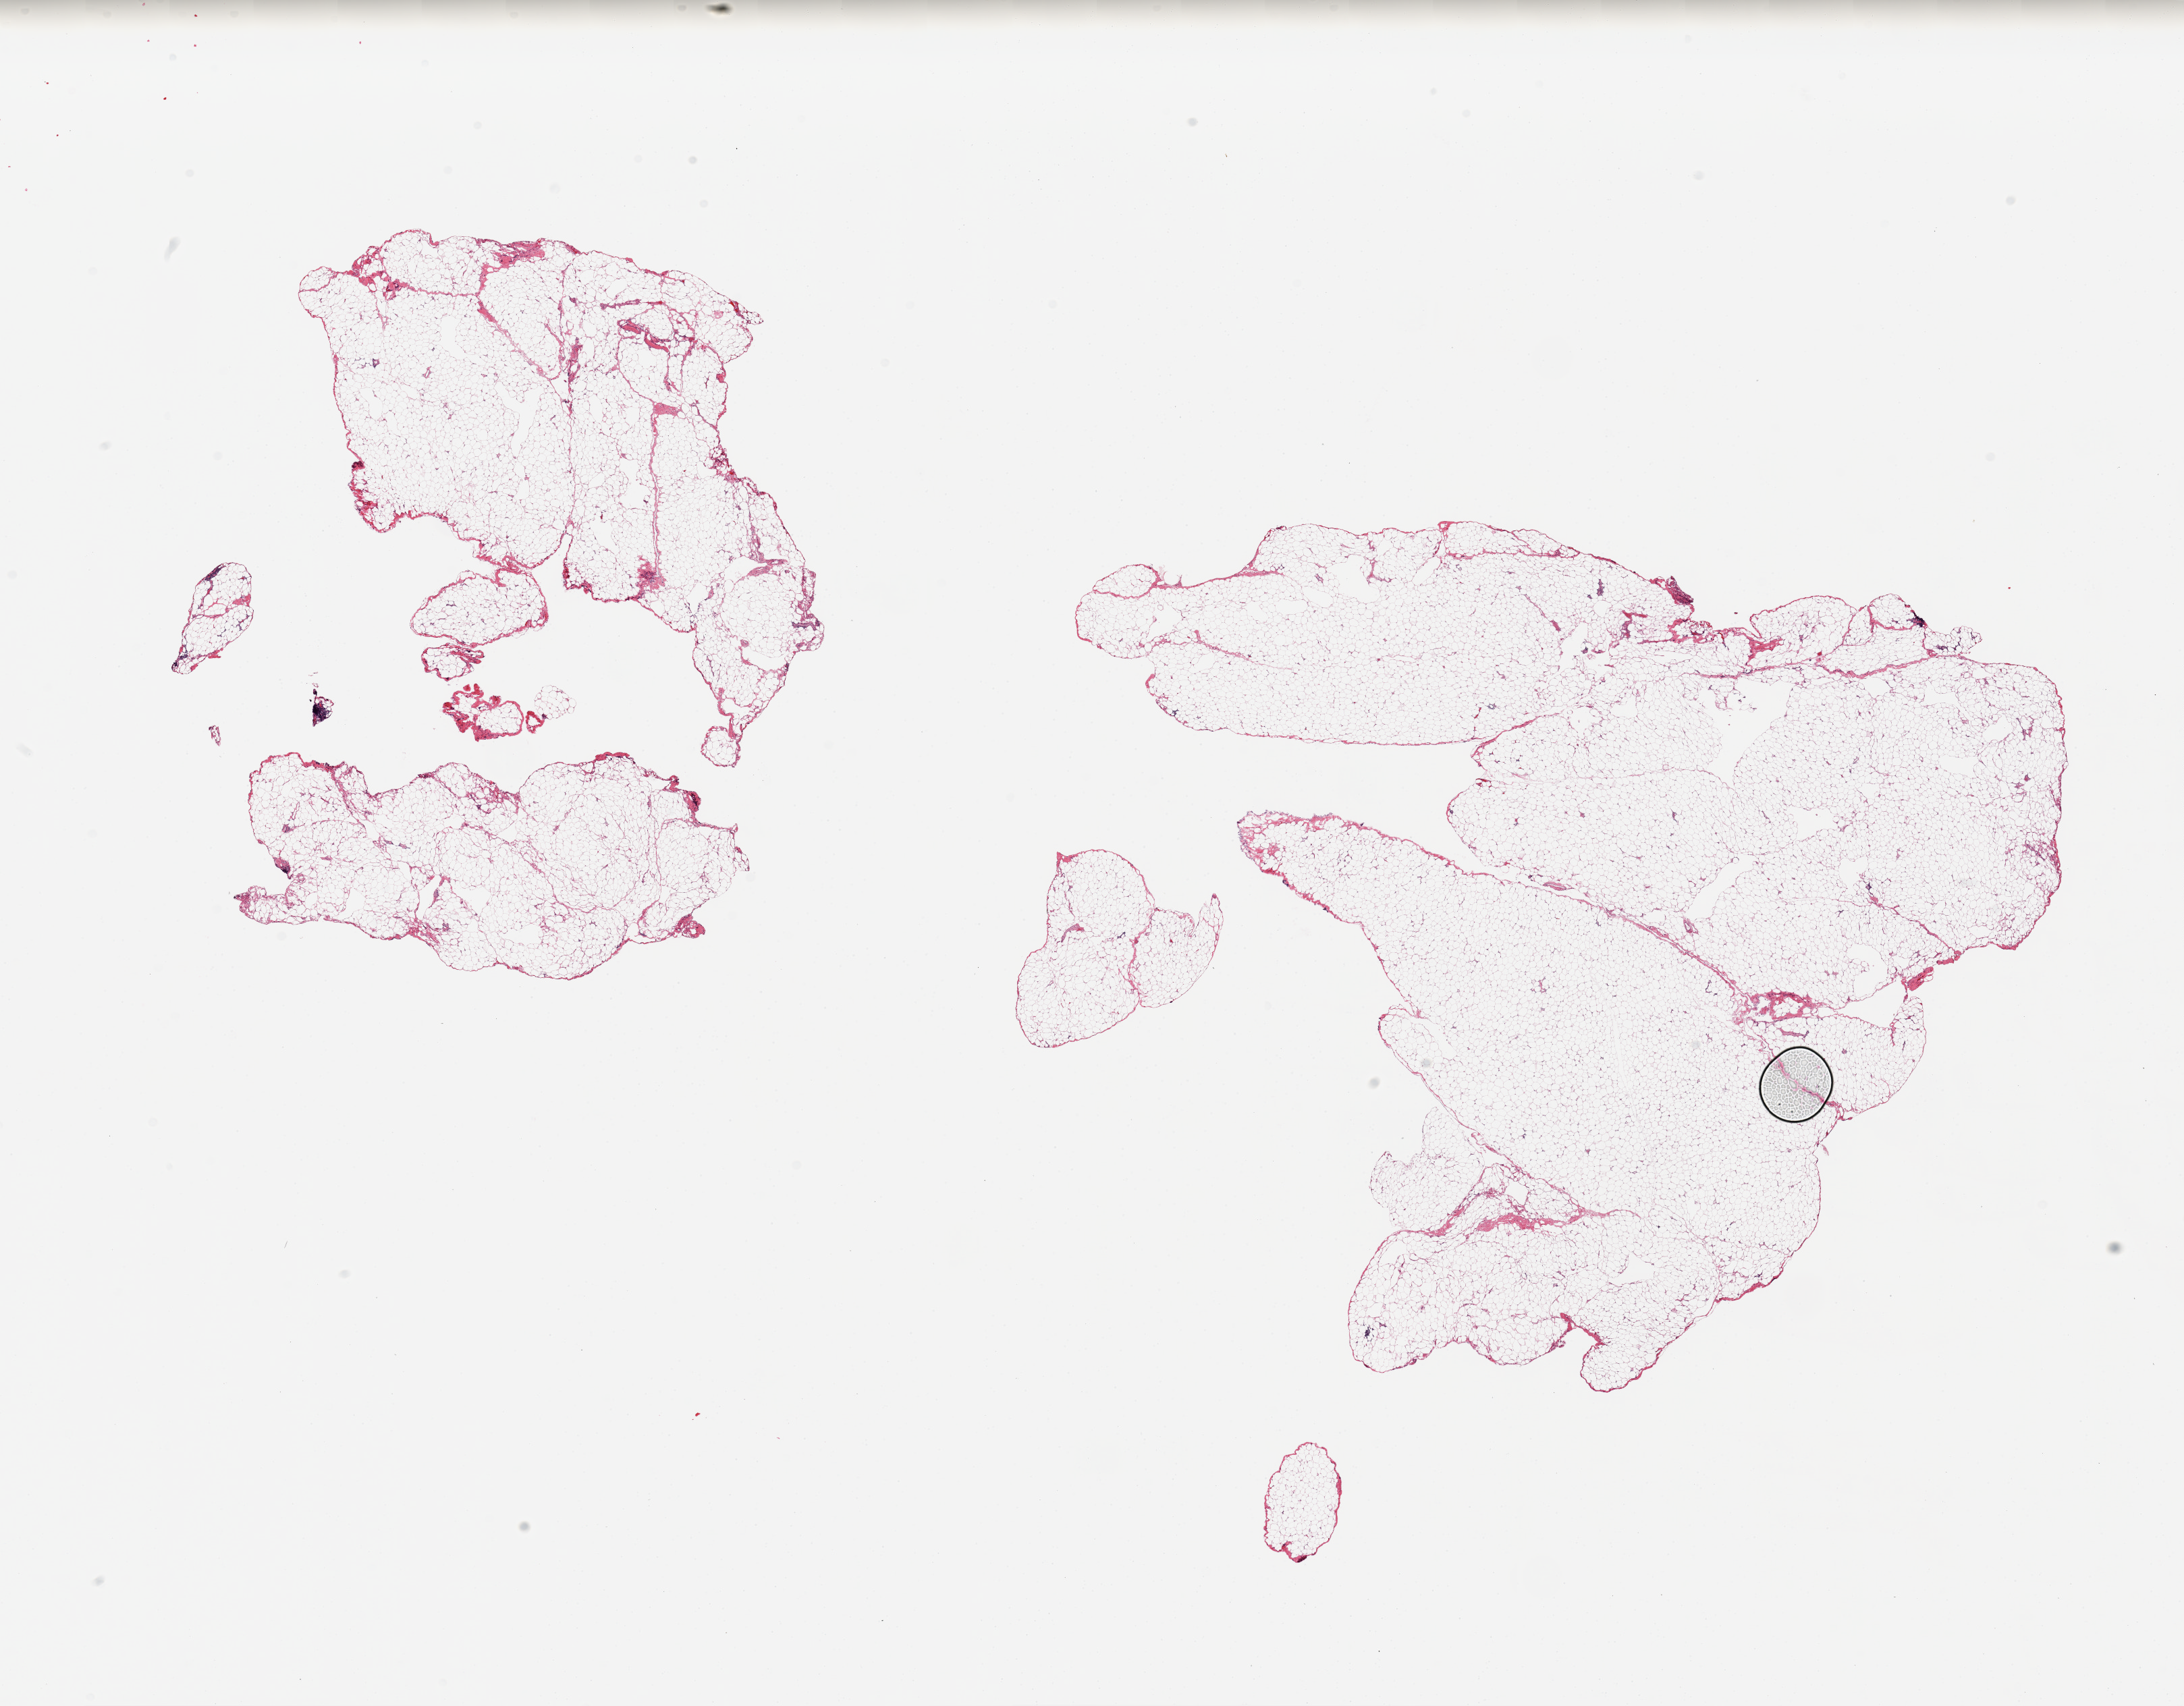
H&E whole-slide image — whole scanned area (about 25.6 x 20.0 mm, from a 20x scan) shown as a low-resolution overview; PAXgene-fixed, paraffin-embedded tissue; sampled site (target tissue): omentum; donor tissue sample. Donor: male.
Reviewer comment on this tissue sample: 2 pieces, minimal fibrosis.